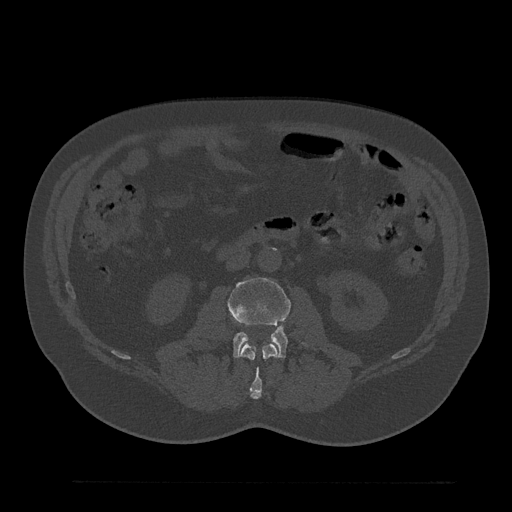
CT including the spine, one axial slice. Slice 62 of 797 in the series (ordered by position). Reconstruction kernel Br40s/3. Bone window (W 1800 / L 400 HU). 0.5 mm slice thickness. 512 × 512 image matrix, field of view 430 × 430 mm. Male patient, age 61 years. From the clinical record (not read from this slice): primary cancer: prostate.
Structures marked on this image (semi-automatically segmented with operator editing):
- L2 vertebra: bounding box <240,344,278,399> (left, top, right, bottom; pixels)
- L3 vertebra: <228,277,306,358>